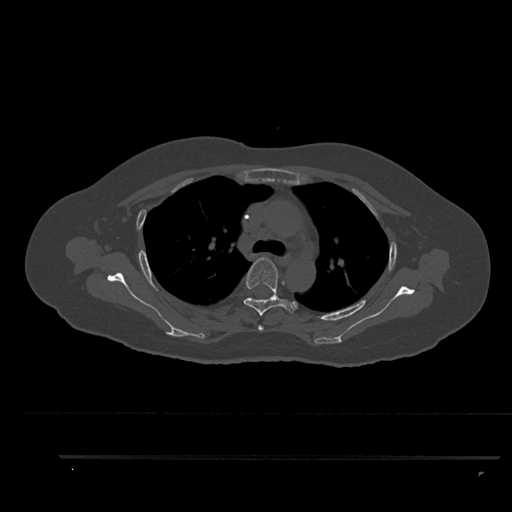
CT including the spine, one axial slice; position 643 of 797 along the scan axis; bone window (W 1800 / L 400 HU); 512 × 512 image matrix, field of view 408 × 408 mm. Female patient, age 44 years. From the clinical record (not read from this slice): primary cancer: renal.
Structures marked on this image (semi-automatically segmented with operator editing):
- T3 vertebra: bounding box [x1, y1, x2, y2] px = [258, 325, 264, 331]
- T4 vertebra: [244, 257, 297, 317]